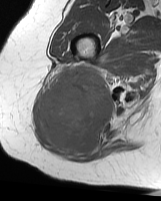
MRI of an extremity soft-tissue mass, one axial slice. MR volume resampled by the dataset authors to the PET/CT grid (not the native acquisition matrix). 161 × 201 image matrix, field of view 157 × 196 mm. Female patient. Case-level facts recorded for this patient, not image findings: histological type: synovial sarcoma; grade: intermediate; site of the primary tumour: right buttock.
Annotated regions visible in this slice (expert contour drawn on MRI and transferred to this co-registered scan by the dataset authors):
- gross tumour volume including surrounding oedema: bounding box [x1, y1, x2, y2] px = [38, 65, 114, 157]
- gross tumour volume (mass): [38, 65, 114, 157]